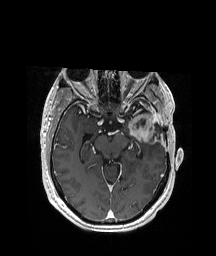
Brain MRI from a brain-tumour surgery series, one axial slice; slice 122 of 208 in the series (ordered by position); T1-weighted post-contrast; 1 mm slice thickness; 216 × 256 image matrix, field of view 228 × 270 mm. From the clinical record (not read from this slice): histopathology: Glioblastoma; WHO grade: 4.
Structures marked on this image (expert manual segmentation):
- previous resection cavity: bounding box (x1, y1, x2, y2) in pixels: (136, 119, 162, 133)
- tumour: (123, 109, 158, 140)